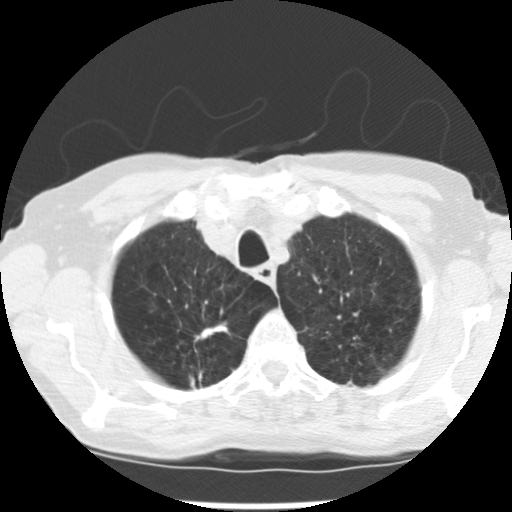
Chest CT (low-dose screening protocol), one axial image. Baseline screening round. Lung window (W 1500 / L -600 HU). Female participant, aged 72 years at enrolment. Current smoker at enrolment.
• Lesion marked by an expert reader, bounding box <181,312,232,351> (left, top, right, bottom; pixels).
• The screening reader recorded 3 non-calcified nodules or masses ≥4 mm on this exam (right upper lobe, left upper lobe, left lower lobe); which of them this box marks is not recorded.
• Official screen result: positive, change unspecified: nodule(s) >= 4 mm or enlarging nodule(s), mass(es), or other non-specific abnormalities suspicious for lung cancer.
• Participant outcome: lung cancer diagnosed 50 days after this screen — adenocarcinoma, NOS, right upper lobe, moderately differentiated (G2), stage IB (AJCC 6th edition), 22 mm at pathology.